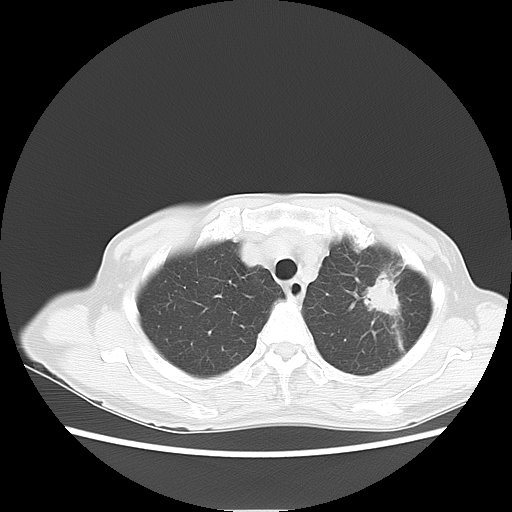
Chest CT, one axial slice. Slice 9 of 13 in the series (ordered by position). Reconstruction kernel LUNG. Lung window (W 1500 / L -600 HU). 5 mm slice thickness. 512 × 512 image matrix, field of view 350 × 350 mm. Female patient, age 71 years. From the clinical record (not read from this slice): clinical TNM (as recorded): T2 N0 M0.
Outlined on this slice (rectangle marked by the reading radiologist):
- lung tumour (recorded histology: adenocarcinoma): bounding box (x1, y1, x2, y2) in pixels: (358, 270, 406, 322)